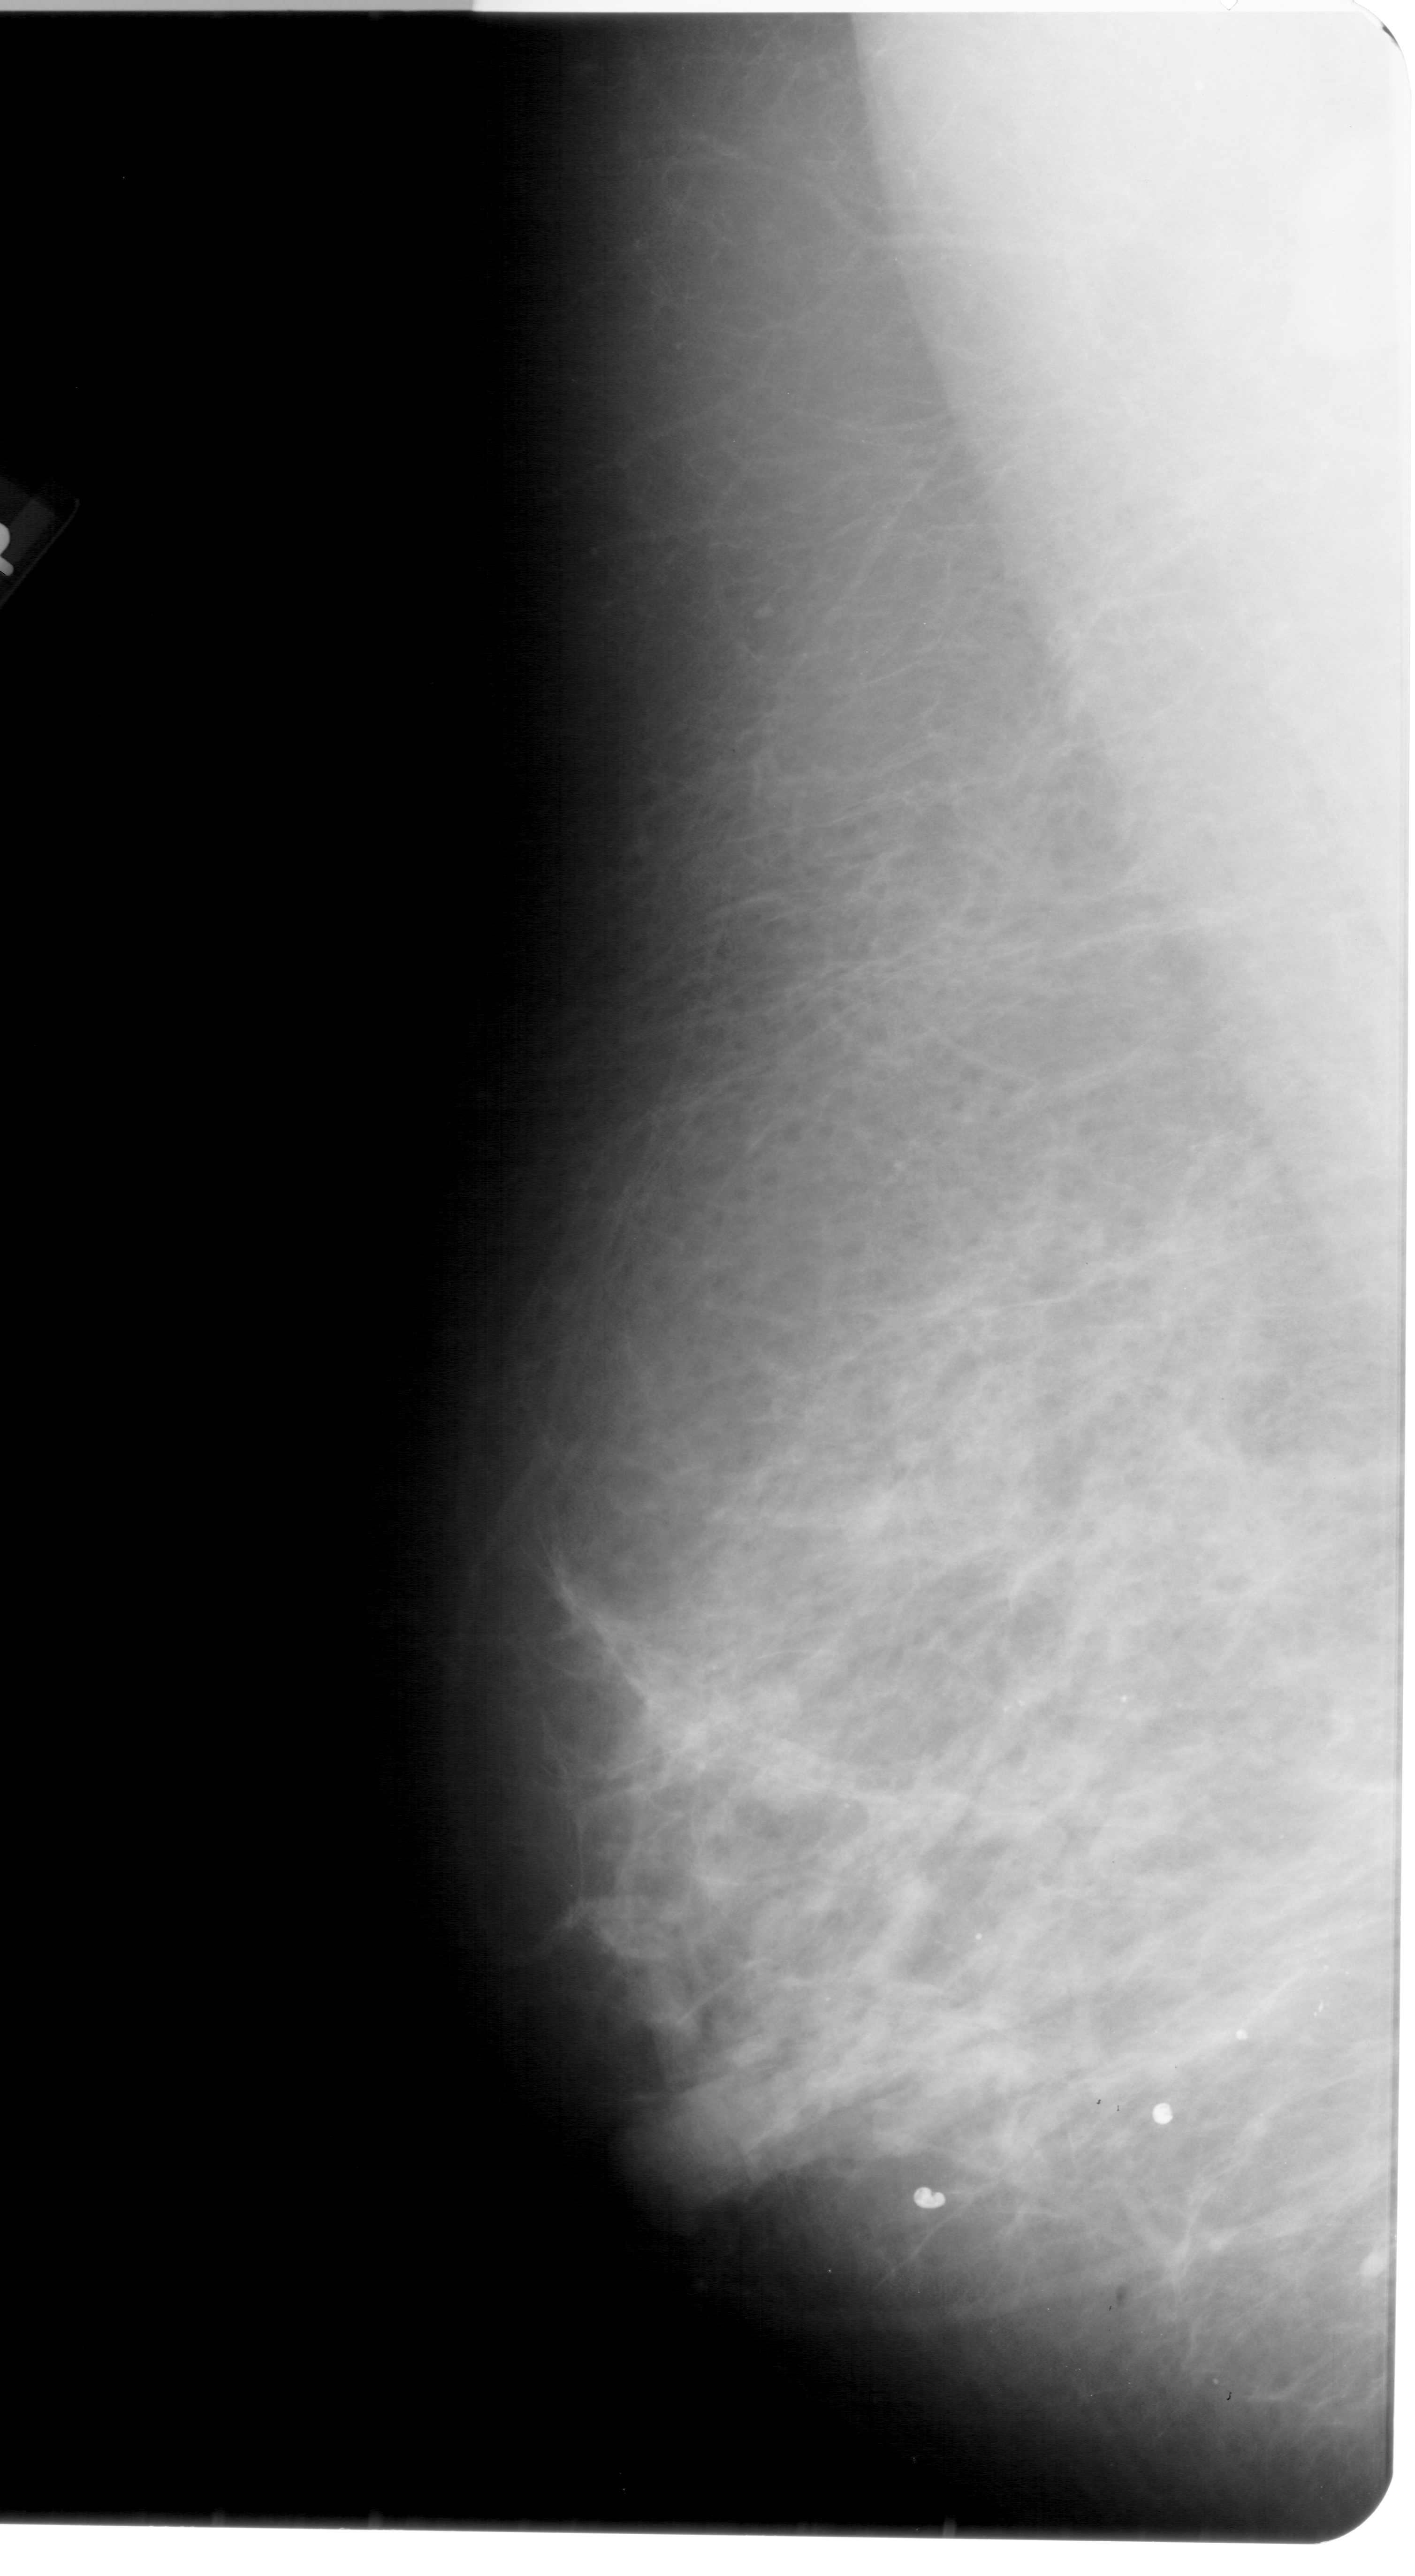
Digitized screen-film mammogram. Left breast. Mediolateral oblique (MLO) view. BI-RADS breast density category 2 (scale 1–4). 1415 × 2576 image matrix.
Expert-marked regions of interest on this film, with their recorded descriptors:
- calcifications, morphology pleomorphic, distribution clustered; BI-RADS assessment category 4; pathology (as recorded): benign: bounding box [x1, y1, x2, y2] px = [1293, 1938, 1355, 2022]